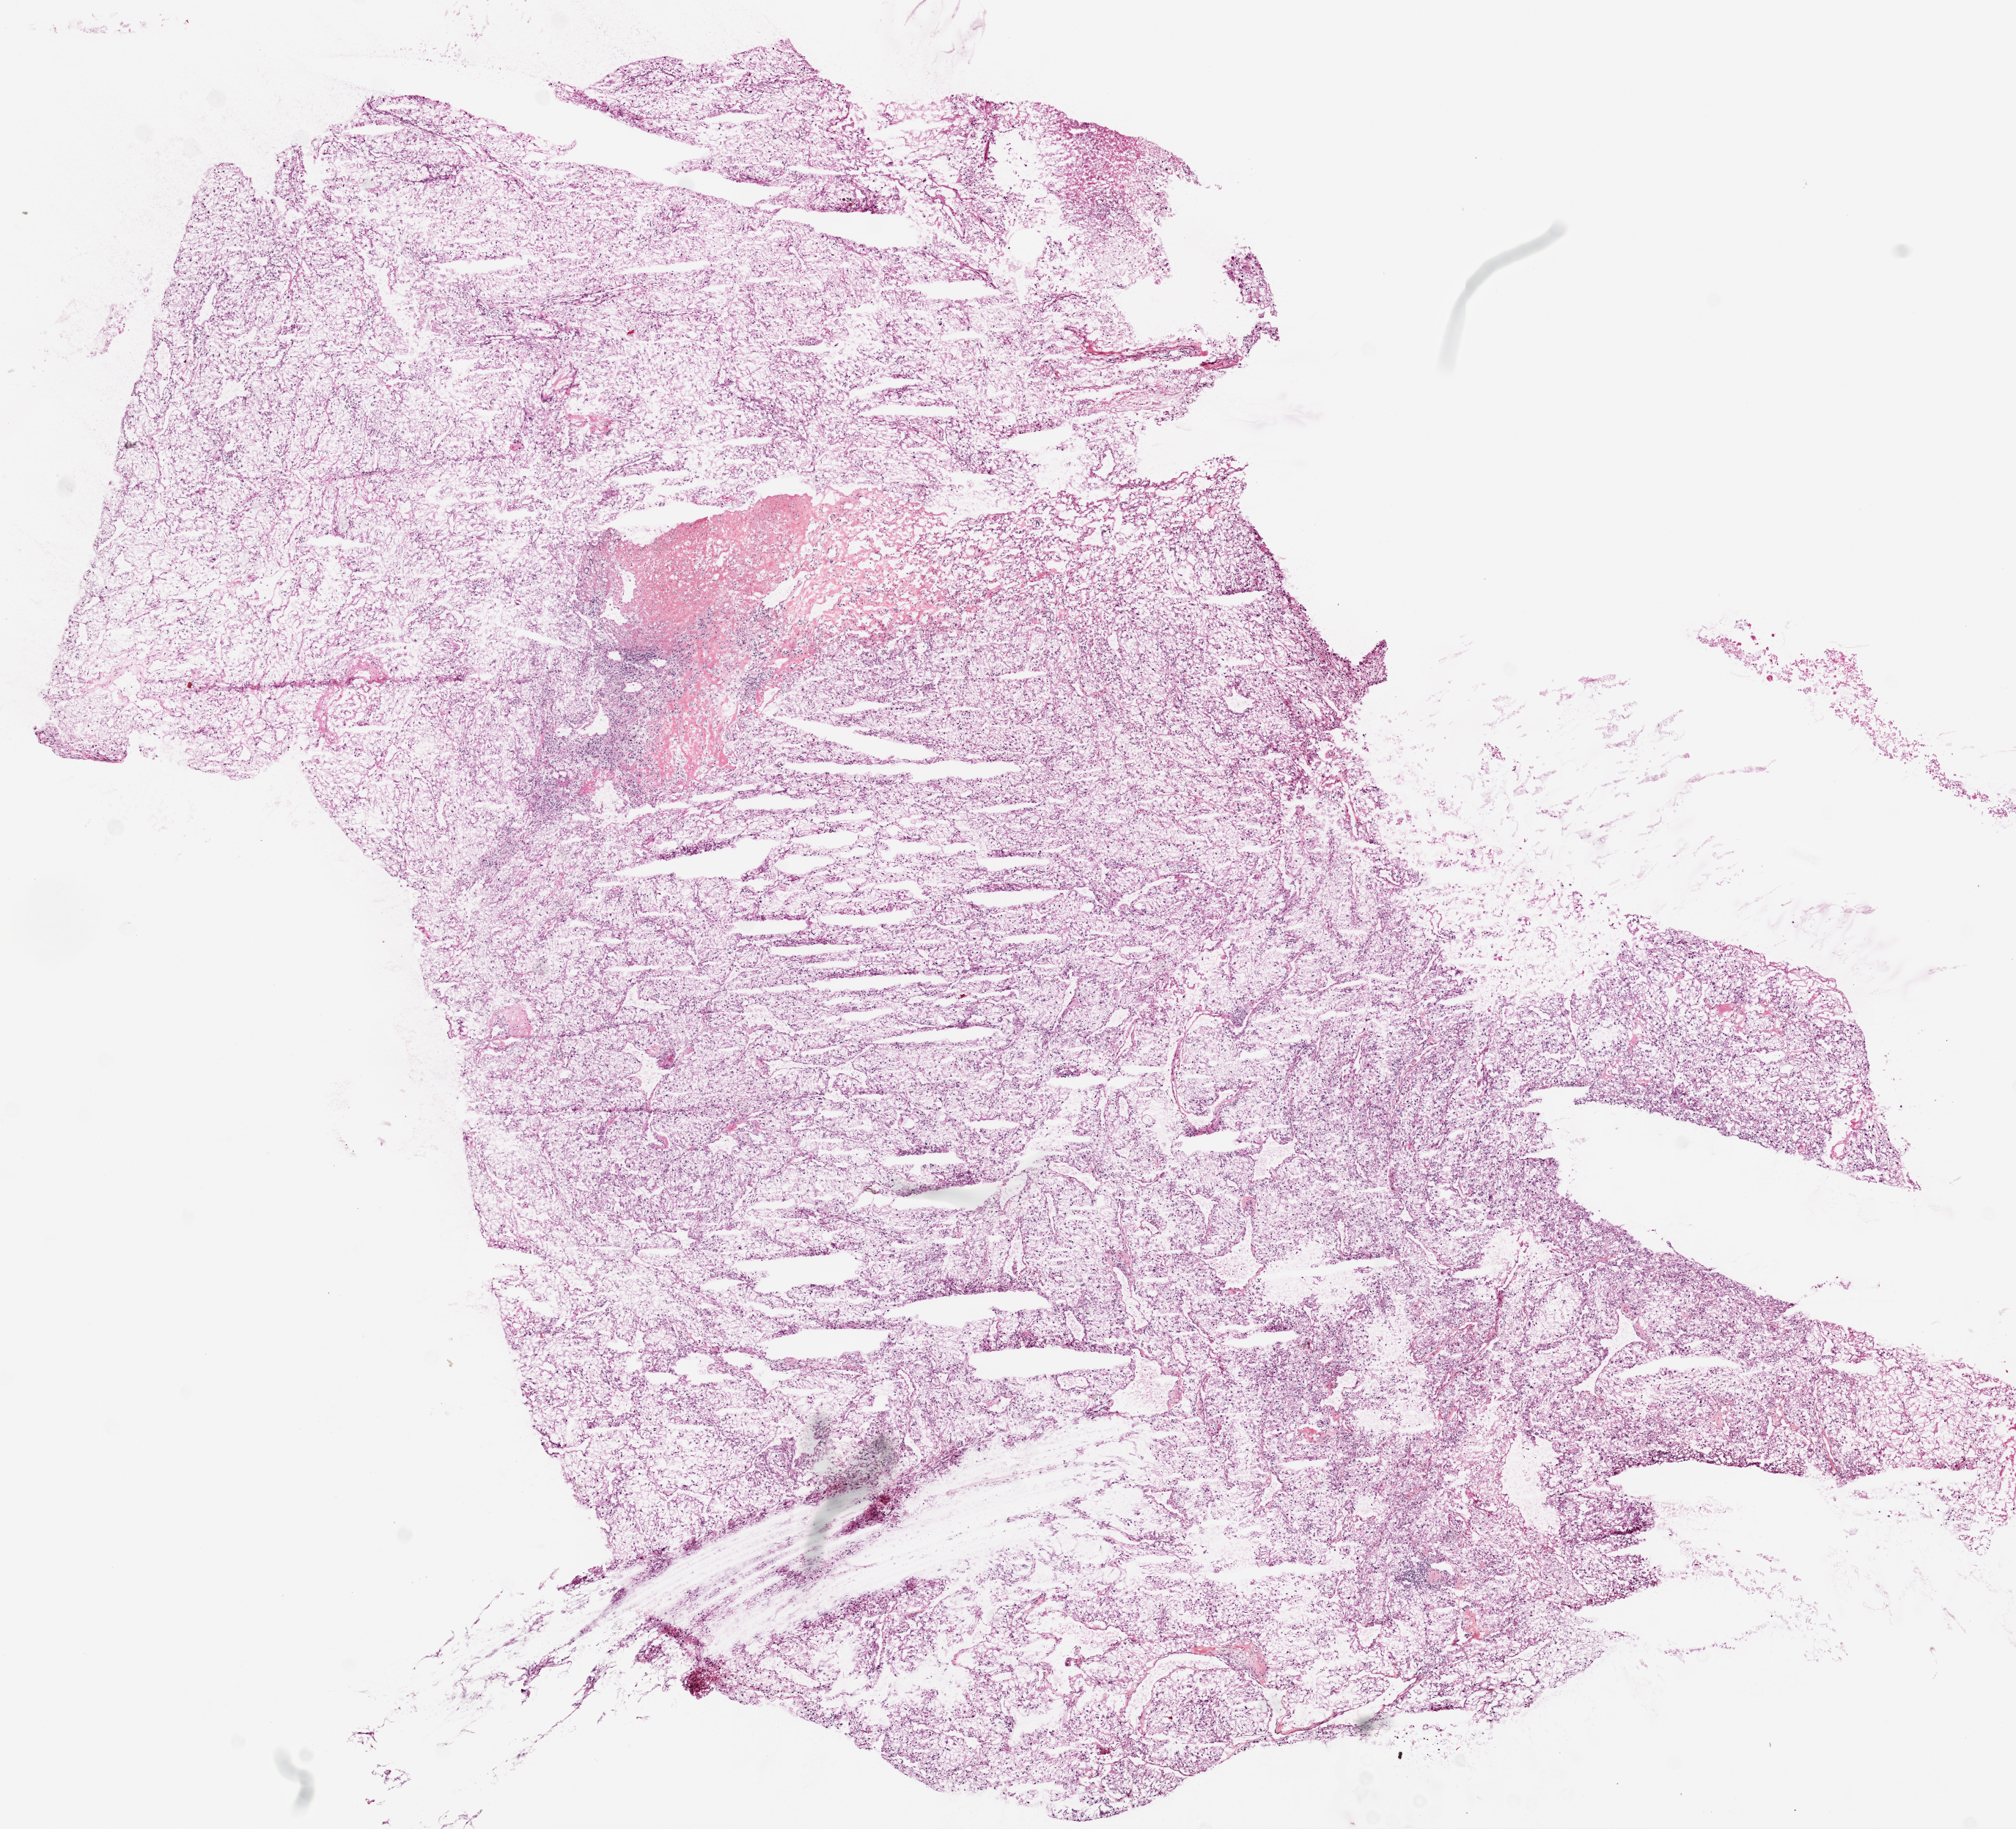
Whole-slide histology image, H&E, shown as a low-resolution overview of the whole scanned area (about 11.0 x 10.0 mm, acquisition: 20x scan); frozen section from the top of the tissue portion; sample: primary tumour, kidney. Male patient; age at initial diagnosis 65 years. Histologic grade: G2 (moderately differentiated). Slide review estimates, as recorded: tumour cells 100%, tumour nuclei 90%, normal cells 0%, stromal cells 0%, necrosis 0%. Inflammatory infiltration, as recorded: lymphocyte infiltration 1%, monocyte infiltration 0%, neutrophil infiltration 0%.
Laterality: left. AJCC pathologic stage: III (7th edition). Pathologic diagnosis: Clear cell adenocarcinoma, NOS.